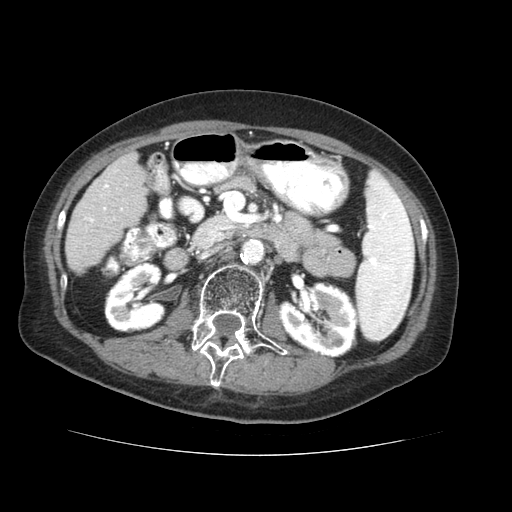
Contrast-enhanced abdominal CT (liver protocol), one axial slice. Slice 13 of 73 in the series (ordered by position). 120 kVp. Soft-tissue window (W 400 / L 40 HU). 2.5 mm slice thickness. 512 × 512 image matrix, field of view 360 × 360 mm. From the clinical record (not read from this slice): diagnosis: hepatocellular carcinoma (patient treated with transarterial chemoembolisation; whether this scan precedes or follows treatment is not stated here); TNM stage (as recorded): Stage-IVB; Child-Pugh class: A; tumour differentiation: well differentiated.
Annotated regions visible in this slice (semi-automatic segmentation, software-assisted and operator-edited):
- liver parenchyma outside the tumour (the mass and vessels are separate outlines, so this box may not span the whole liver): bounding box <66,152,144,272> (left, top, right, bottom; pixels)
- liver vessels: <114,170,118,172>